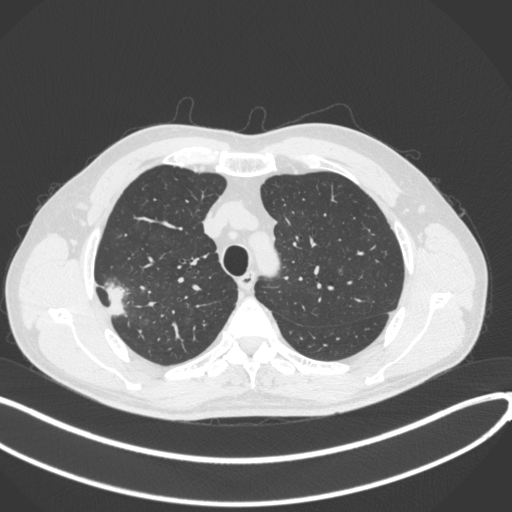
Chest CT, one axial slice. Slice 326 of 381 in the series (ordered by position). Reconstruction kernel B31f. 120 kVp. Lung window (W 1500 / L -600 HU). 512 × 512 image matrix, field of view 400 × 400 mm. Male patient, age 62 years. From the clinical record (not read from this slice): clinical TNM (as recorded): T1c N0 M0; histopathological grade: G2-3.
Structures marked on this image (bounding box drawn by a radiologist):
- lung tumour (recorded histology: adenocarcinoma): bounding box <101,282,130,319> (left, top, right, bottom; pixels)